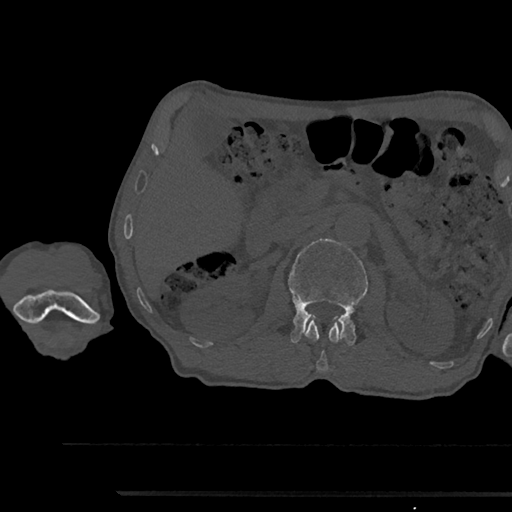
CT including the spine, one axial slice. Position 596 of 797 along the scan axis. Bone window (W 1800 / L 400 HU). 0.5 mm slice thickness. 512 × 512 image matrix. Male patient, age 79 years. From the clinical record (not read from this slice): primary cancer: prostate.
Annotated regions visible in this slice (semi-automatically segmented with operator editing):
- L1 vertebra: box from (x=305, y=319) to (x=343, y=371) px
- L2 vertebra: (x=289, y=239)–(x=367, y=345)